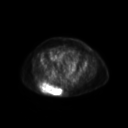
FDG PET of an extremity soft-tissue mass (from a PET/CT study), one axial slice; slice 70 of 267 in the series (ordered by position); 3.27 mm slice thickness; 128 × 128 image matrix, field of view 600 × 600 mm. Female patient, age 60 years. Case-level facts recorded for this patient, not image findings: histological type: spindle cell suggestive of myxofibrosarcoma; grade: intermediate; site of the primary tumour: right buttock.
Outlined on this slice (expert contour drawn on MRI and transferred to this co-registered scan by the dataset authors):
- gross tumour volume (mass): bounding box [x1, y1, x2, y2] px = [37, 81, 63, 96]